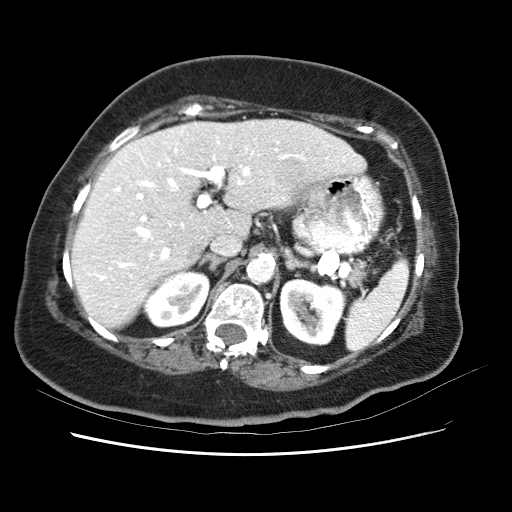
Contrast-enhanced abdominal CT (liver protocol), one axial slice. Slice 39 of 62 in the series (ordered by position). Reconstruction kernel STANDARD. 120 kVp. Soft-tissue window (W 400 / L 40 HU). 2.5 mm slice thickness. 512 × 512 image matrix, field of view 340 × 340 mm. From the clinical record (not read from this slice): diagnosis: hepatocellular carcinoma (patient treated with transarterial chemoembolisation; whether this scan precedes or follows treatment is not stated here); TNM stage (as recorded): Stage-I; Child-Pugh class: B; tumour size: 5.3 cm.
Annotated regions visible in this slice (semi-automatic segmentation, software-assisted and operator-edited):
- liver parenchyma outside the tumour (the mass and vessels are separate outlines, so this box may not span the whole liver): bounding box [x1, y1, x2, y2] px = [72, 117, 364, 328]
- mass: [260, 145, 322, 214]
- liver vessels: [96, 128, 283, 304]